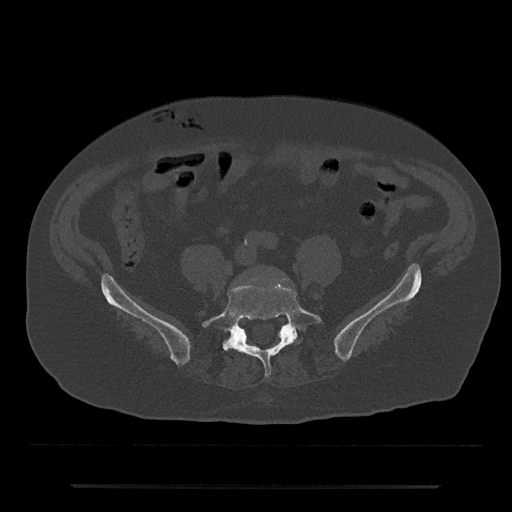
CT including the spine, one axial slice. Slice 291 of 797 in the series (ordered by position). Bone window (W 1800 / L 400 HU). 0.5 mm slice thickness. 512 × 512 image matrix, field of view 434 × 434 mm. Male patient, age 80 years. From the clinical record (not read from this slice): primary cancer: prostate; vertebrae with lytic lesions (as recorded): L1, T11.
Annotated regions visible in this slice (semi-automatic segmentation, software-assisted and operator-edited):
- L5 vertebra: box from (x=202, y=285) to (x=321, y=377) px